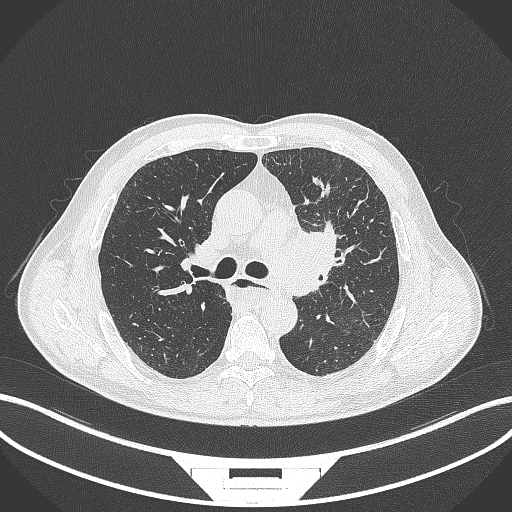
Chest CT, one axial slice; slice 241 of 411 in the series (ordered by position); reconstruction kernel B70f; 120 kVp; lung window (W 1500 / L -600 HU); 512 × 512 image matrix, field of view 400 × 400 mm. Patient: male, 57 years. Case-level facts recorded for this patient, not image findings: clinical TNM (as recorded): T2a N1 M0.
Outlined on this slice (bounding box drawn by a radiologist):
- lung tumour (recorded histology: squamous cell carcinoma): bounding box [x1, y1, x2, y2] px = [273, 220, 349, 303]